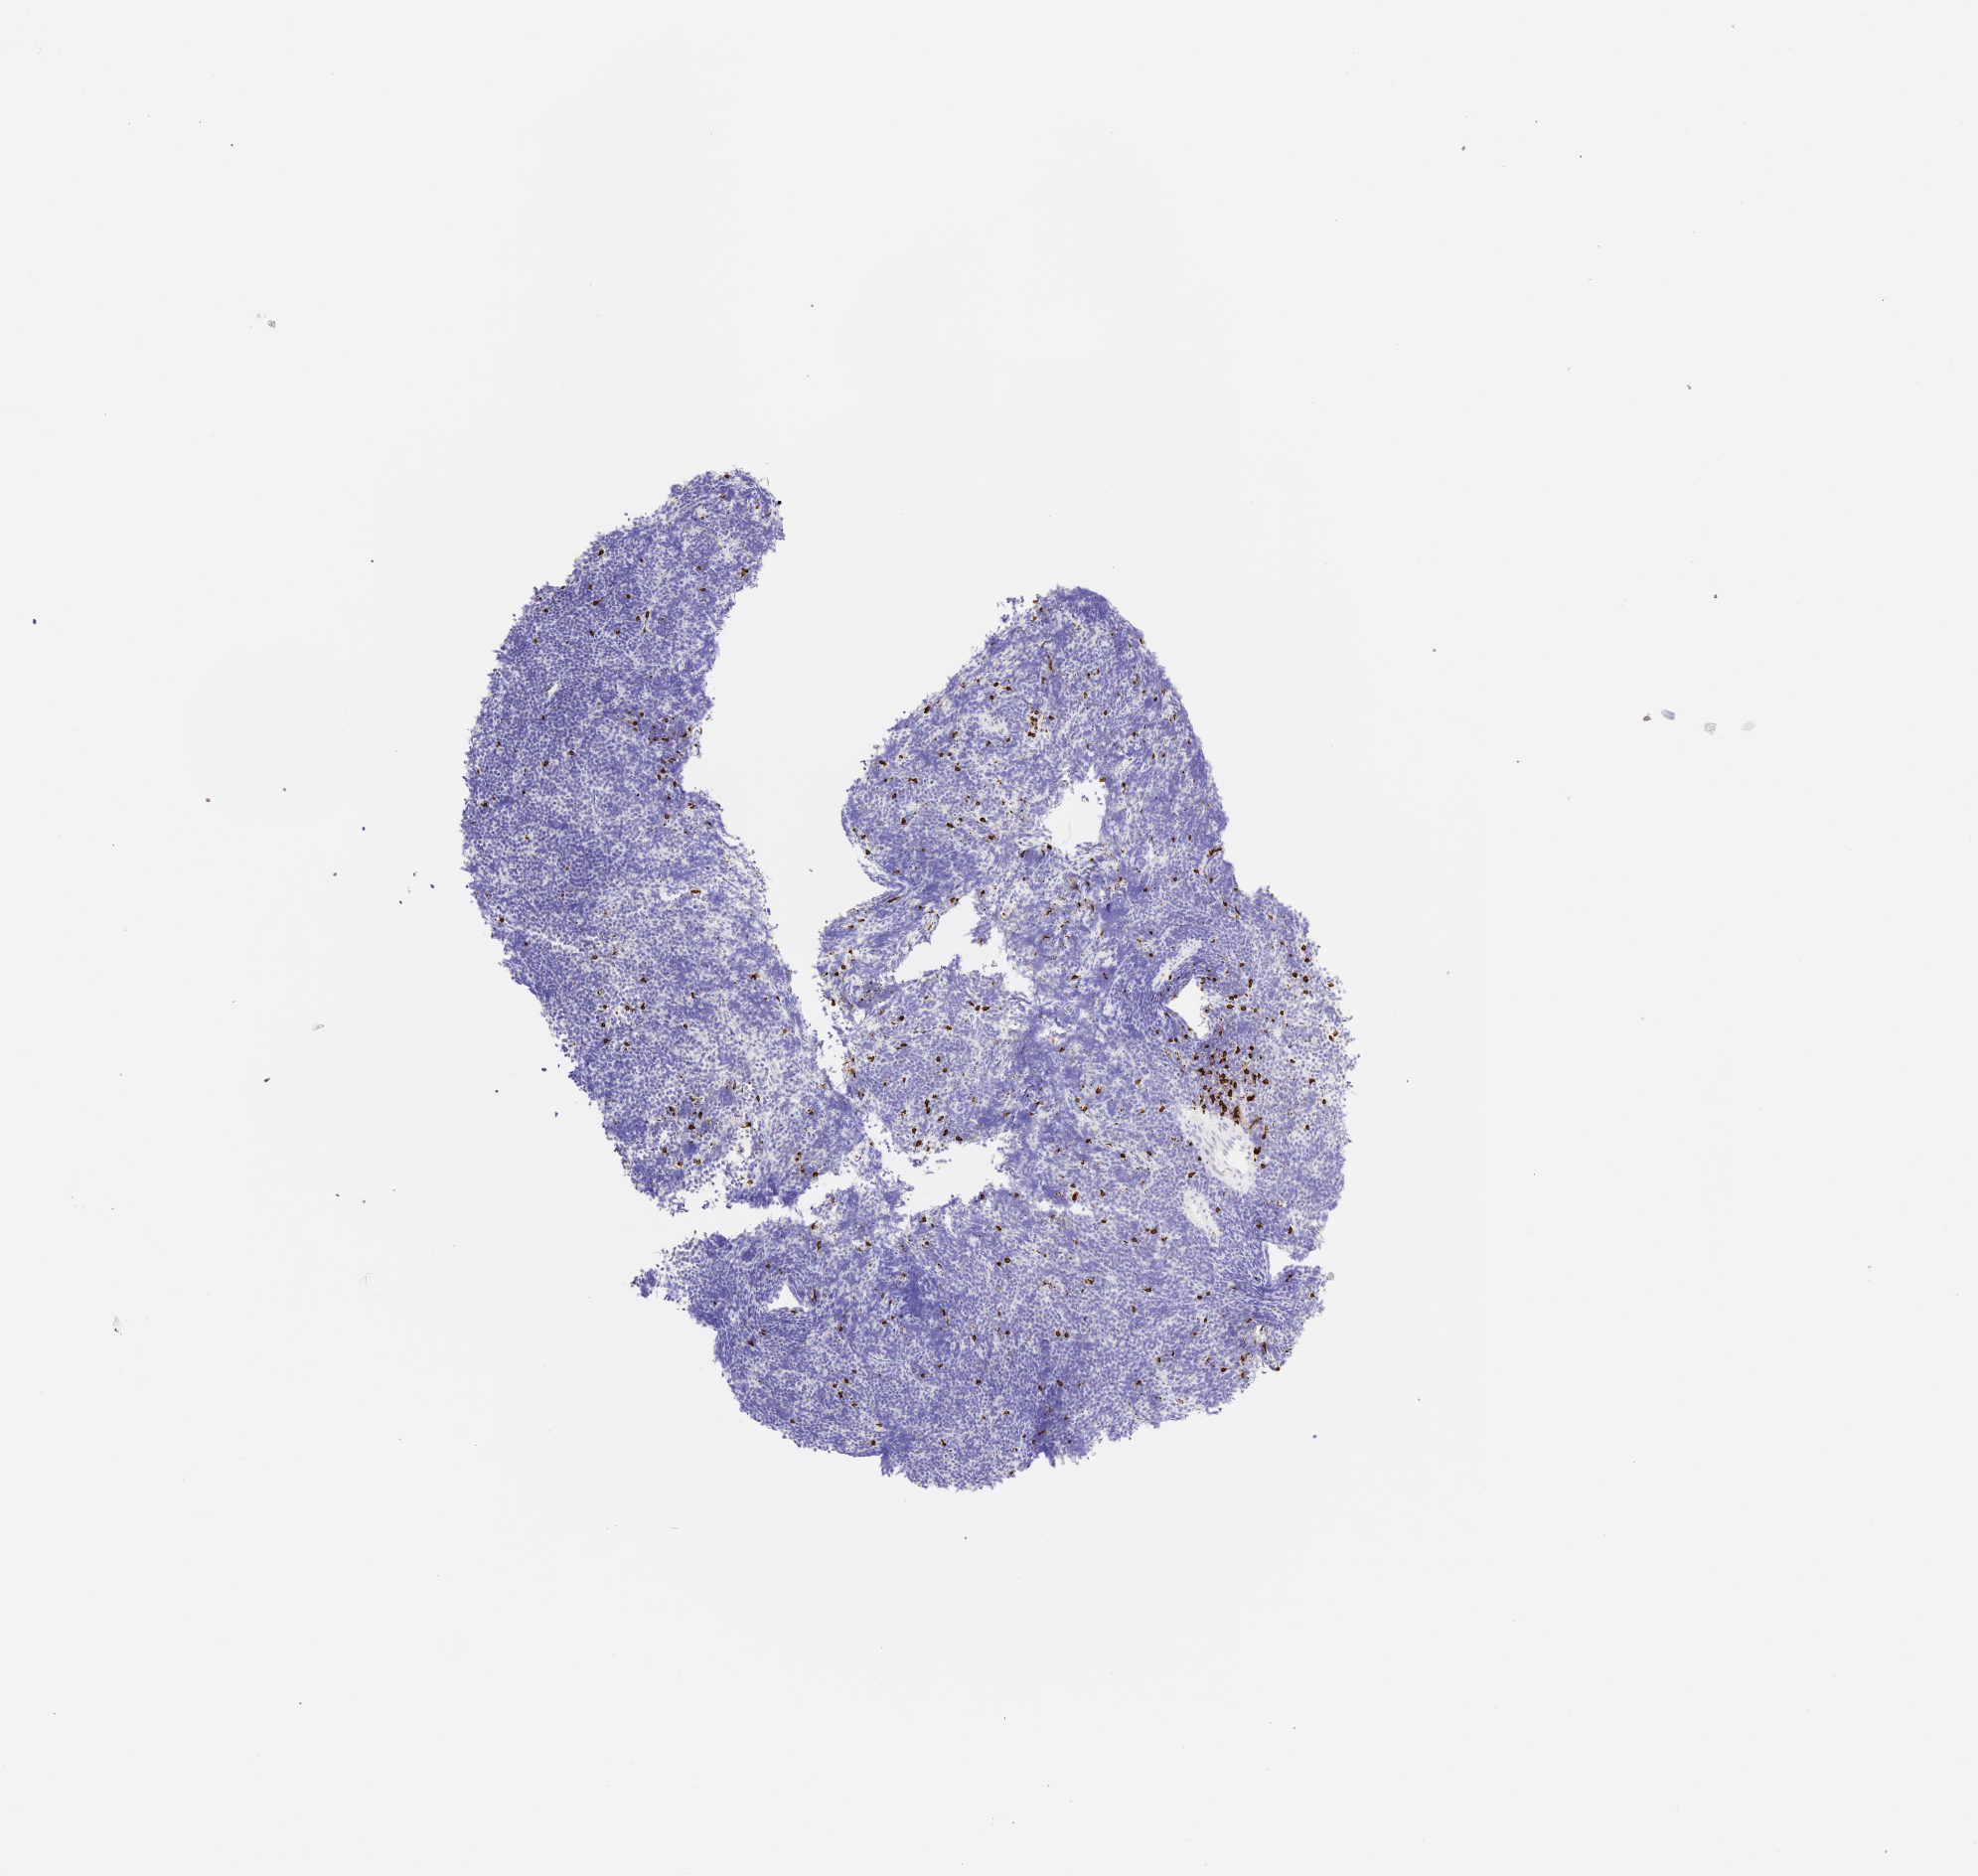
Whole-slide image, immunohistochemical stain for CD3 — a low-resolution overview of the entire scanned area, about 4.0 x 3.8 mm. Tumor tissue. Female patient; age at initial diagnosis 8 years.
- histologic diagnosis: Burkitt lymphoma, NOS